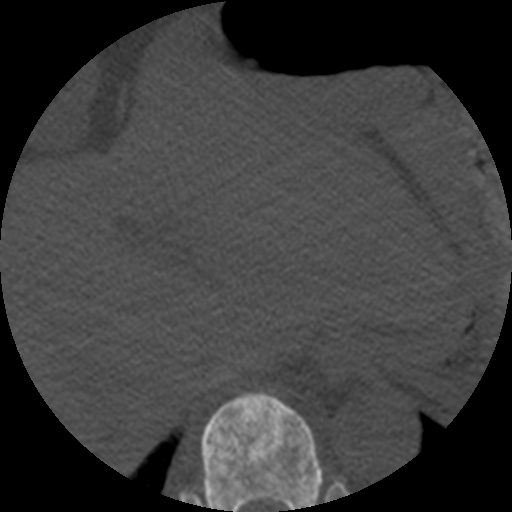
CT including the spine, one axial slice. Slice 270 of 508 in the series (ordered by position). Reconstruction kernel STANDARD. 120 kVp. Bone window (W 1800 / L 400 HU). 1.25 mm slice thickness. 512 × 512 image matrix, field of view 160 × 160 mm. Patient age 57 years. From the clinical record (not read from this slice): primary cancer: prostate.
Structures marked on this image (semi-automatically segmented with operator editing):
- T10 vertebra: bounding box <183,392,322,512> (left, top, right, bottom; pixels)
- T9 vertebra: <322,473,323,477>